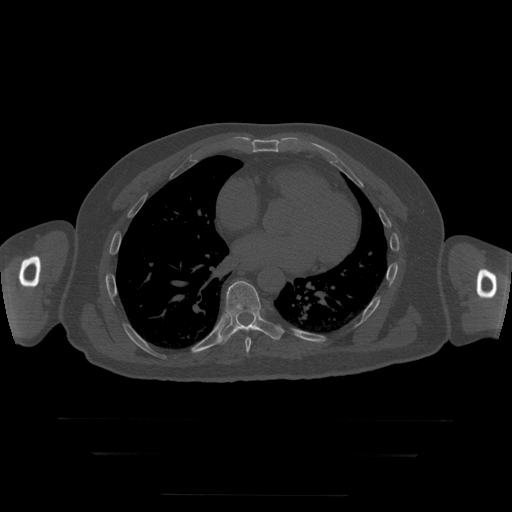
CT including the spine, one axial slice. Slice 150 of 397 in the series (ordered by position). Reconstruction kernel STANDARD. 120 kVp. Bone window (W 1800 / L 400 HU). 1.25 mm slice thickness. 512 × 512 image matrix. Patient age 73 years. From the clinical record (not read from this slice): primary cancer: prostate.
Outlined on this slice (semi-automatically segmented with operator editing):
- T8 vertebra: bounding box <245,338,252,354> (left, top, right, bottom; pixels)
- T9 vertebra: <218,281,284,345>